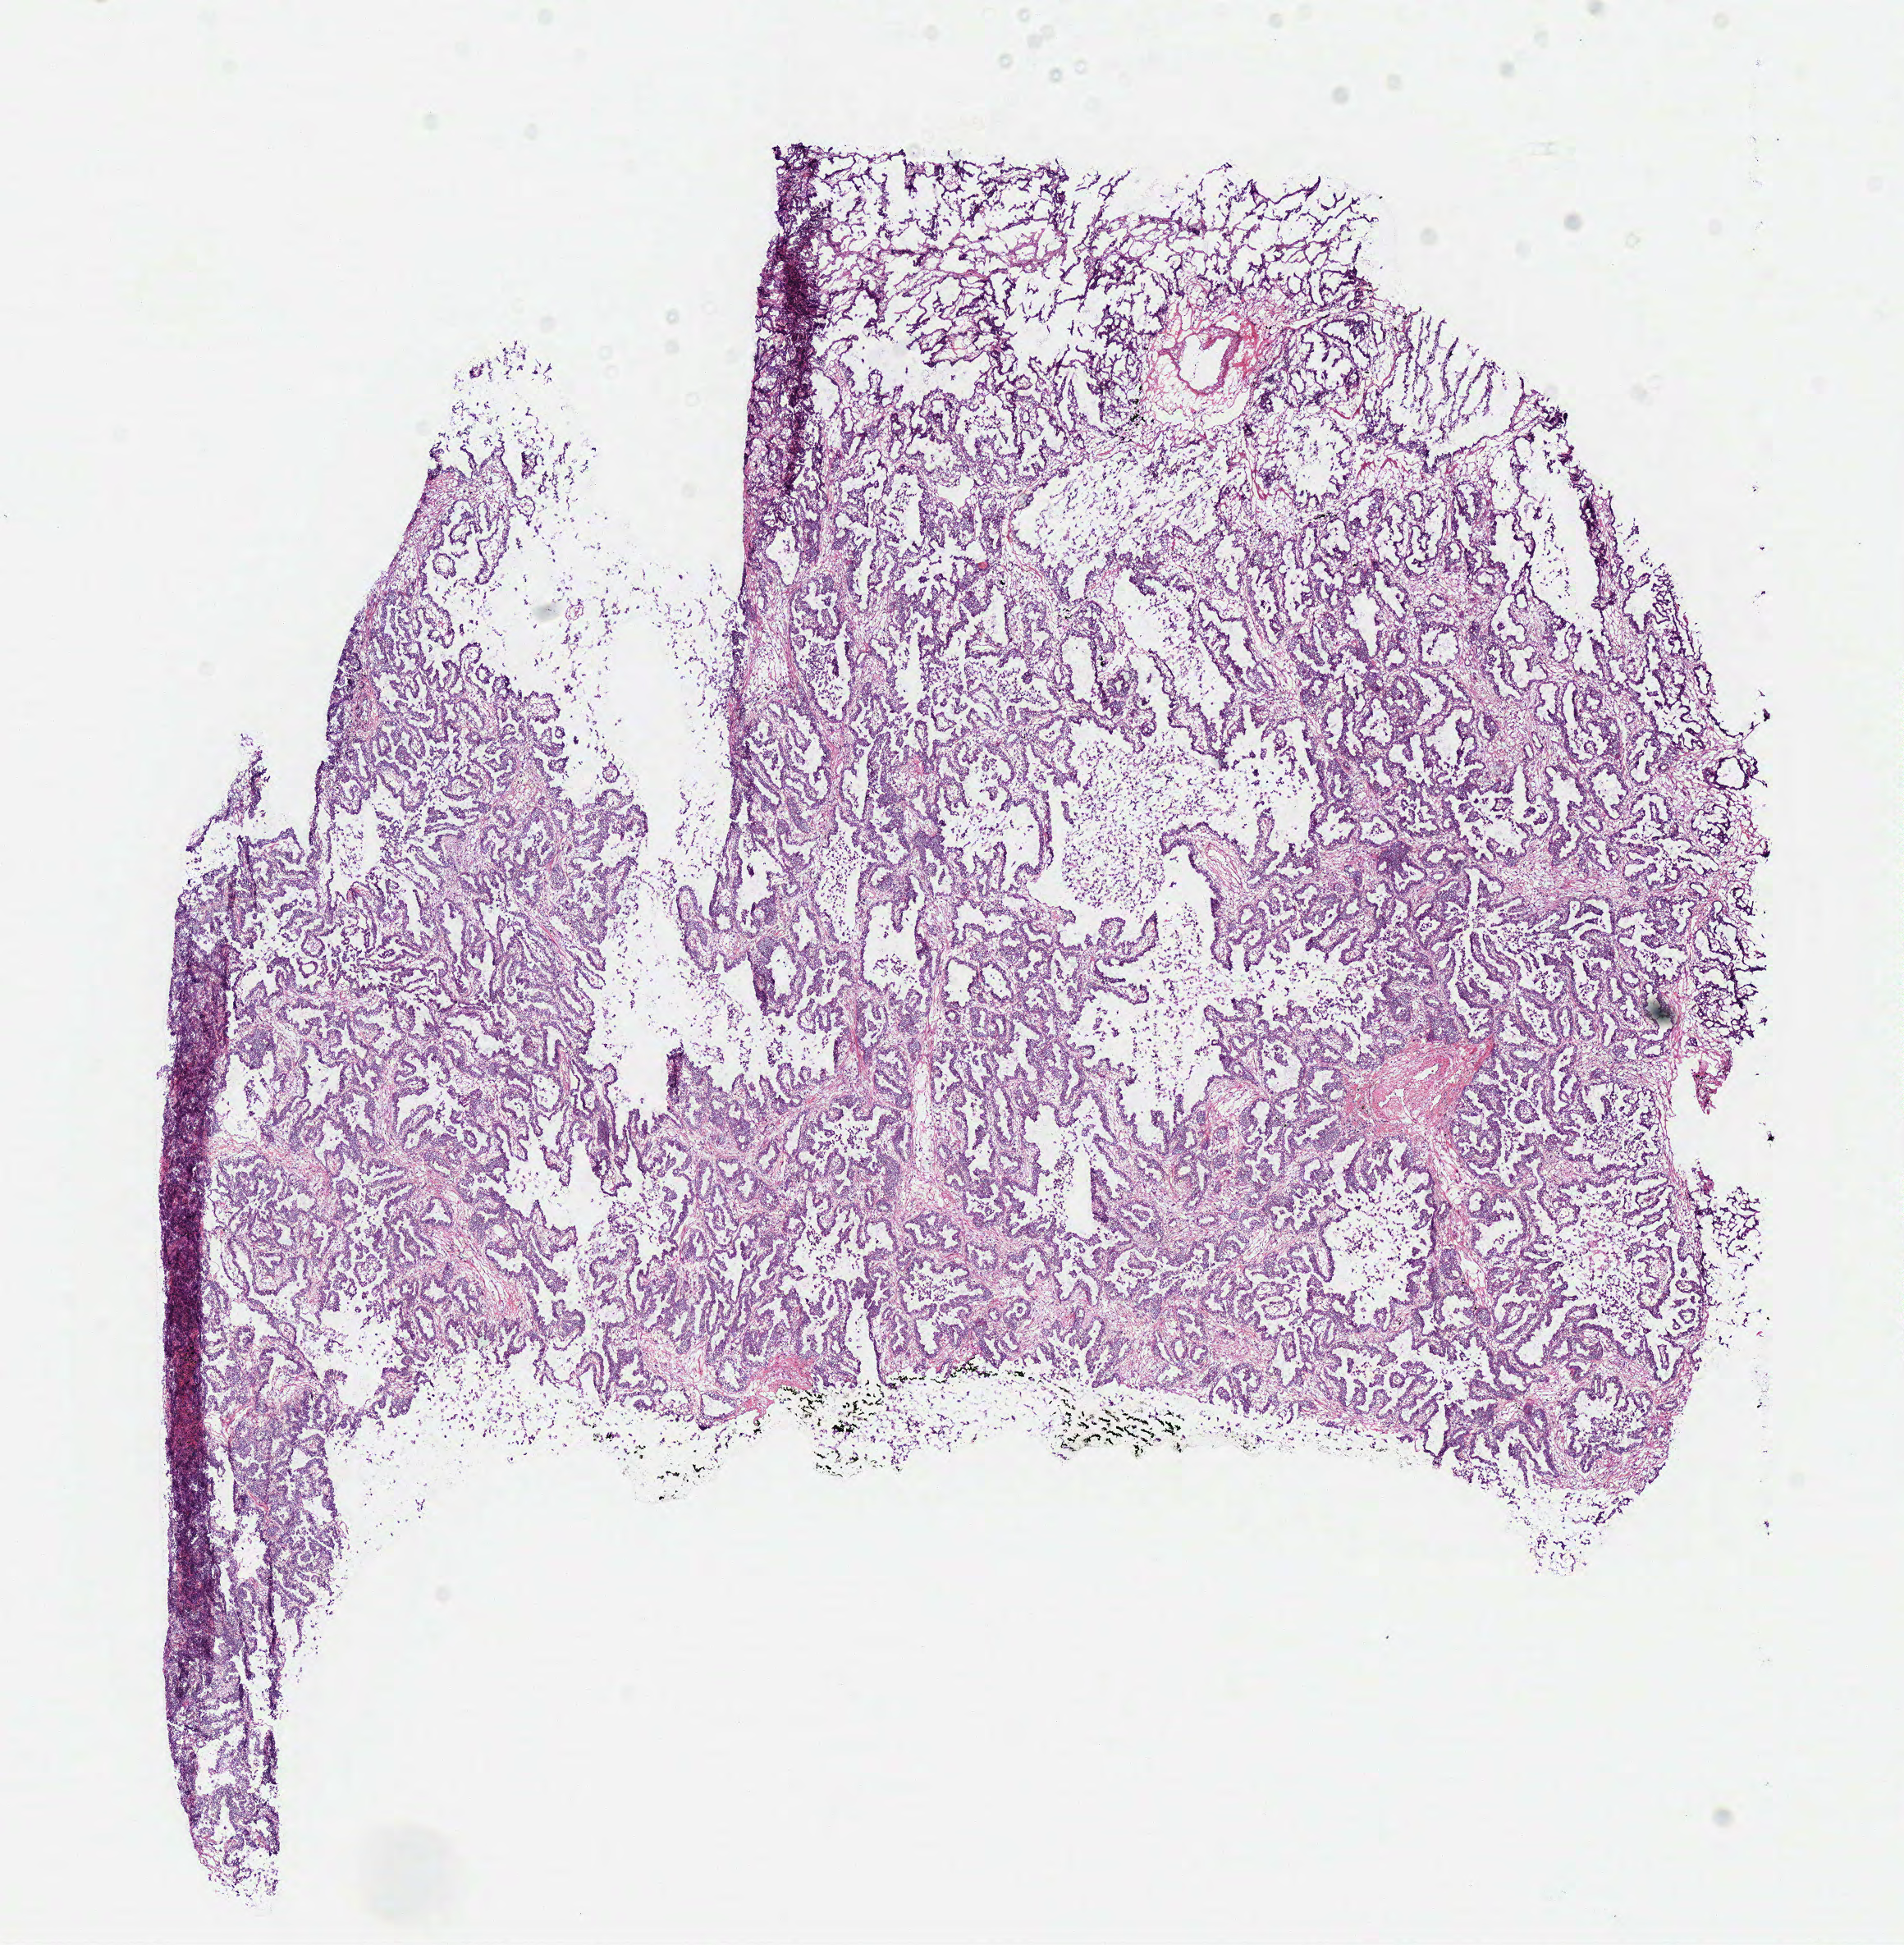
Whole-slide histology image, H&E, low-resolution overview of the scanned area, about 9.1 x 9.3 mm. Frozen section from the bottom of the tissue portion. Sample: primary tumour, lung. Patient: female, age at initial diagnosis 69 years.
Diagnosis: Adenocarcinoma with mixed subtypes (upper lobe, lung).